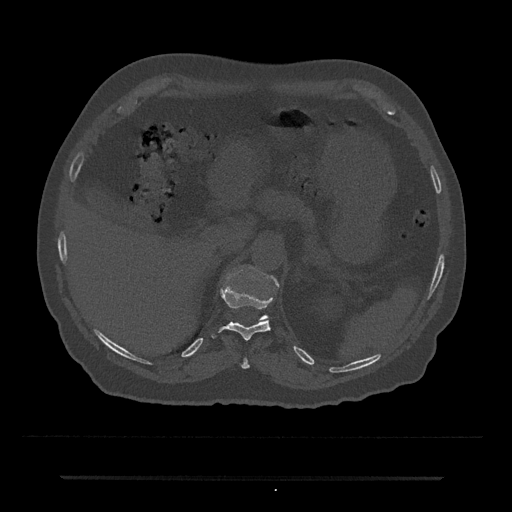
CT including the spine, one axial slice. 120 kVp. Bone window (W 1800 / L 400 HU). 0.5 mm slice thickness. 512 × 512 image matrix, field of view 437 × 437 mm. Male patient, age 69 years. From the clinical record (not read from this slice): primary cancer: prostate.
Annotated regions visible in this slice (semi-automatically segmented with operator editing):
- T10 vertebra: box from (x=240, y=357) to (x=250, y=369) px
- T11 vertebra: (x=211, y=287)–(x=273, y=340)
- T12 vertebra: (x=261, y=276)–(x=279, y=320)